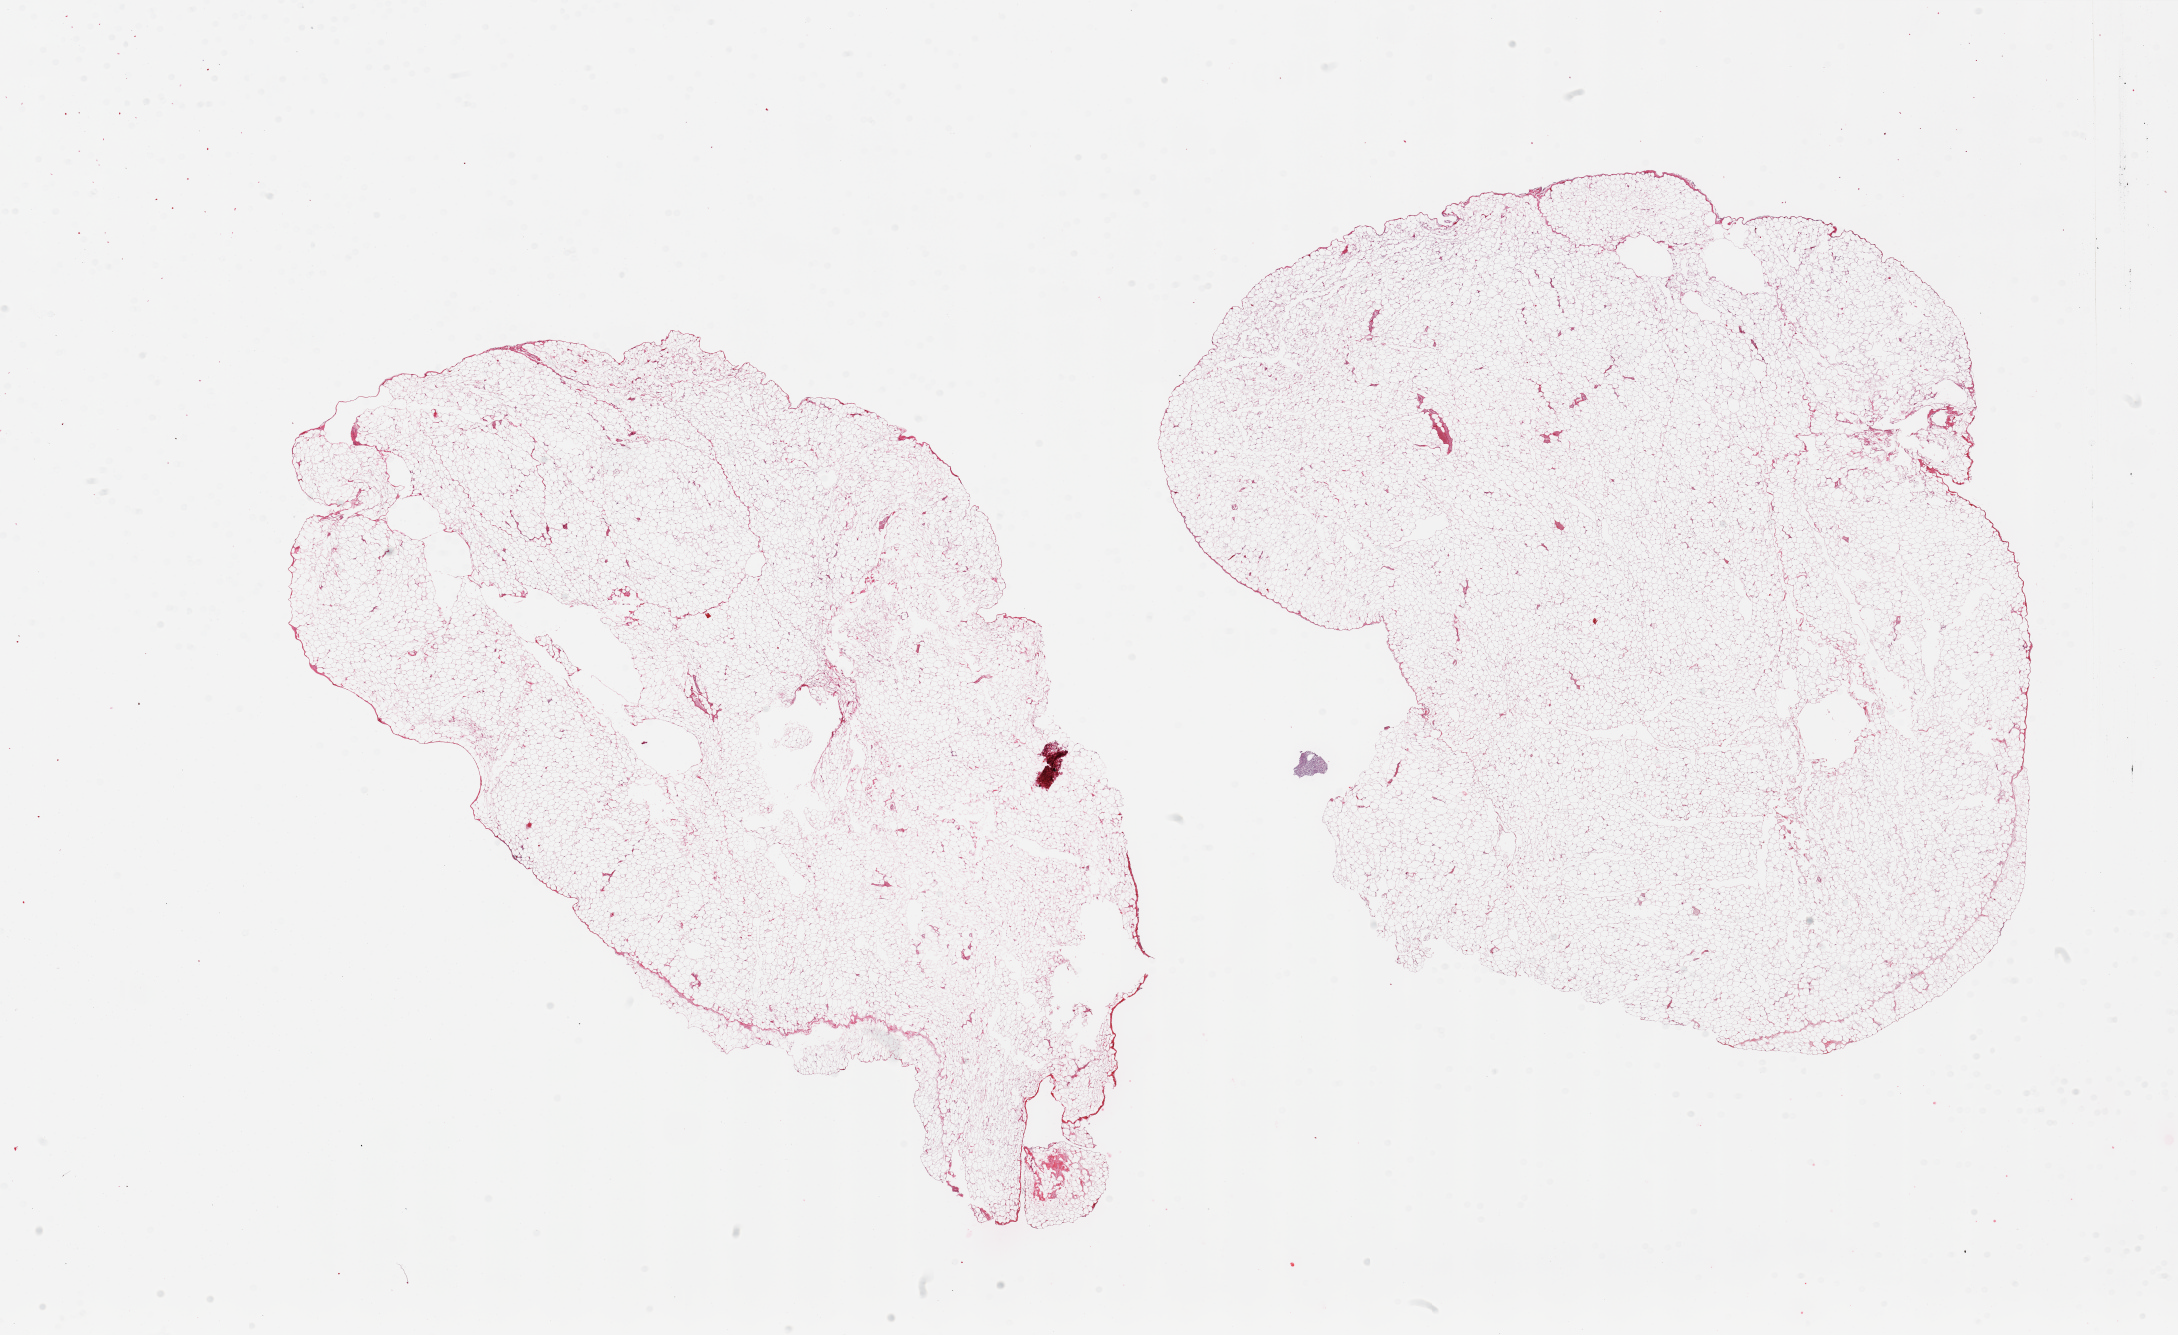
Digitized hematoxylin and eosin (H&E)-stained section — a low-resolution overview of the entire scanned area, about 34.5 x 21.1 mm, PAXgene-fixed, paraffin-embedded tissue, section of omentum (target tissue), donor tissue sample. Donor: male.
Reviewer comment on this tissue sample: 2 pieces.